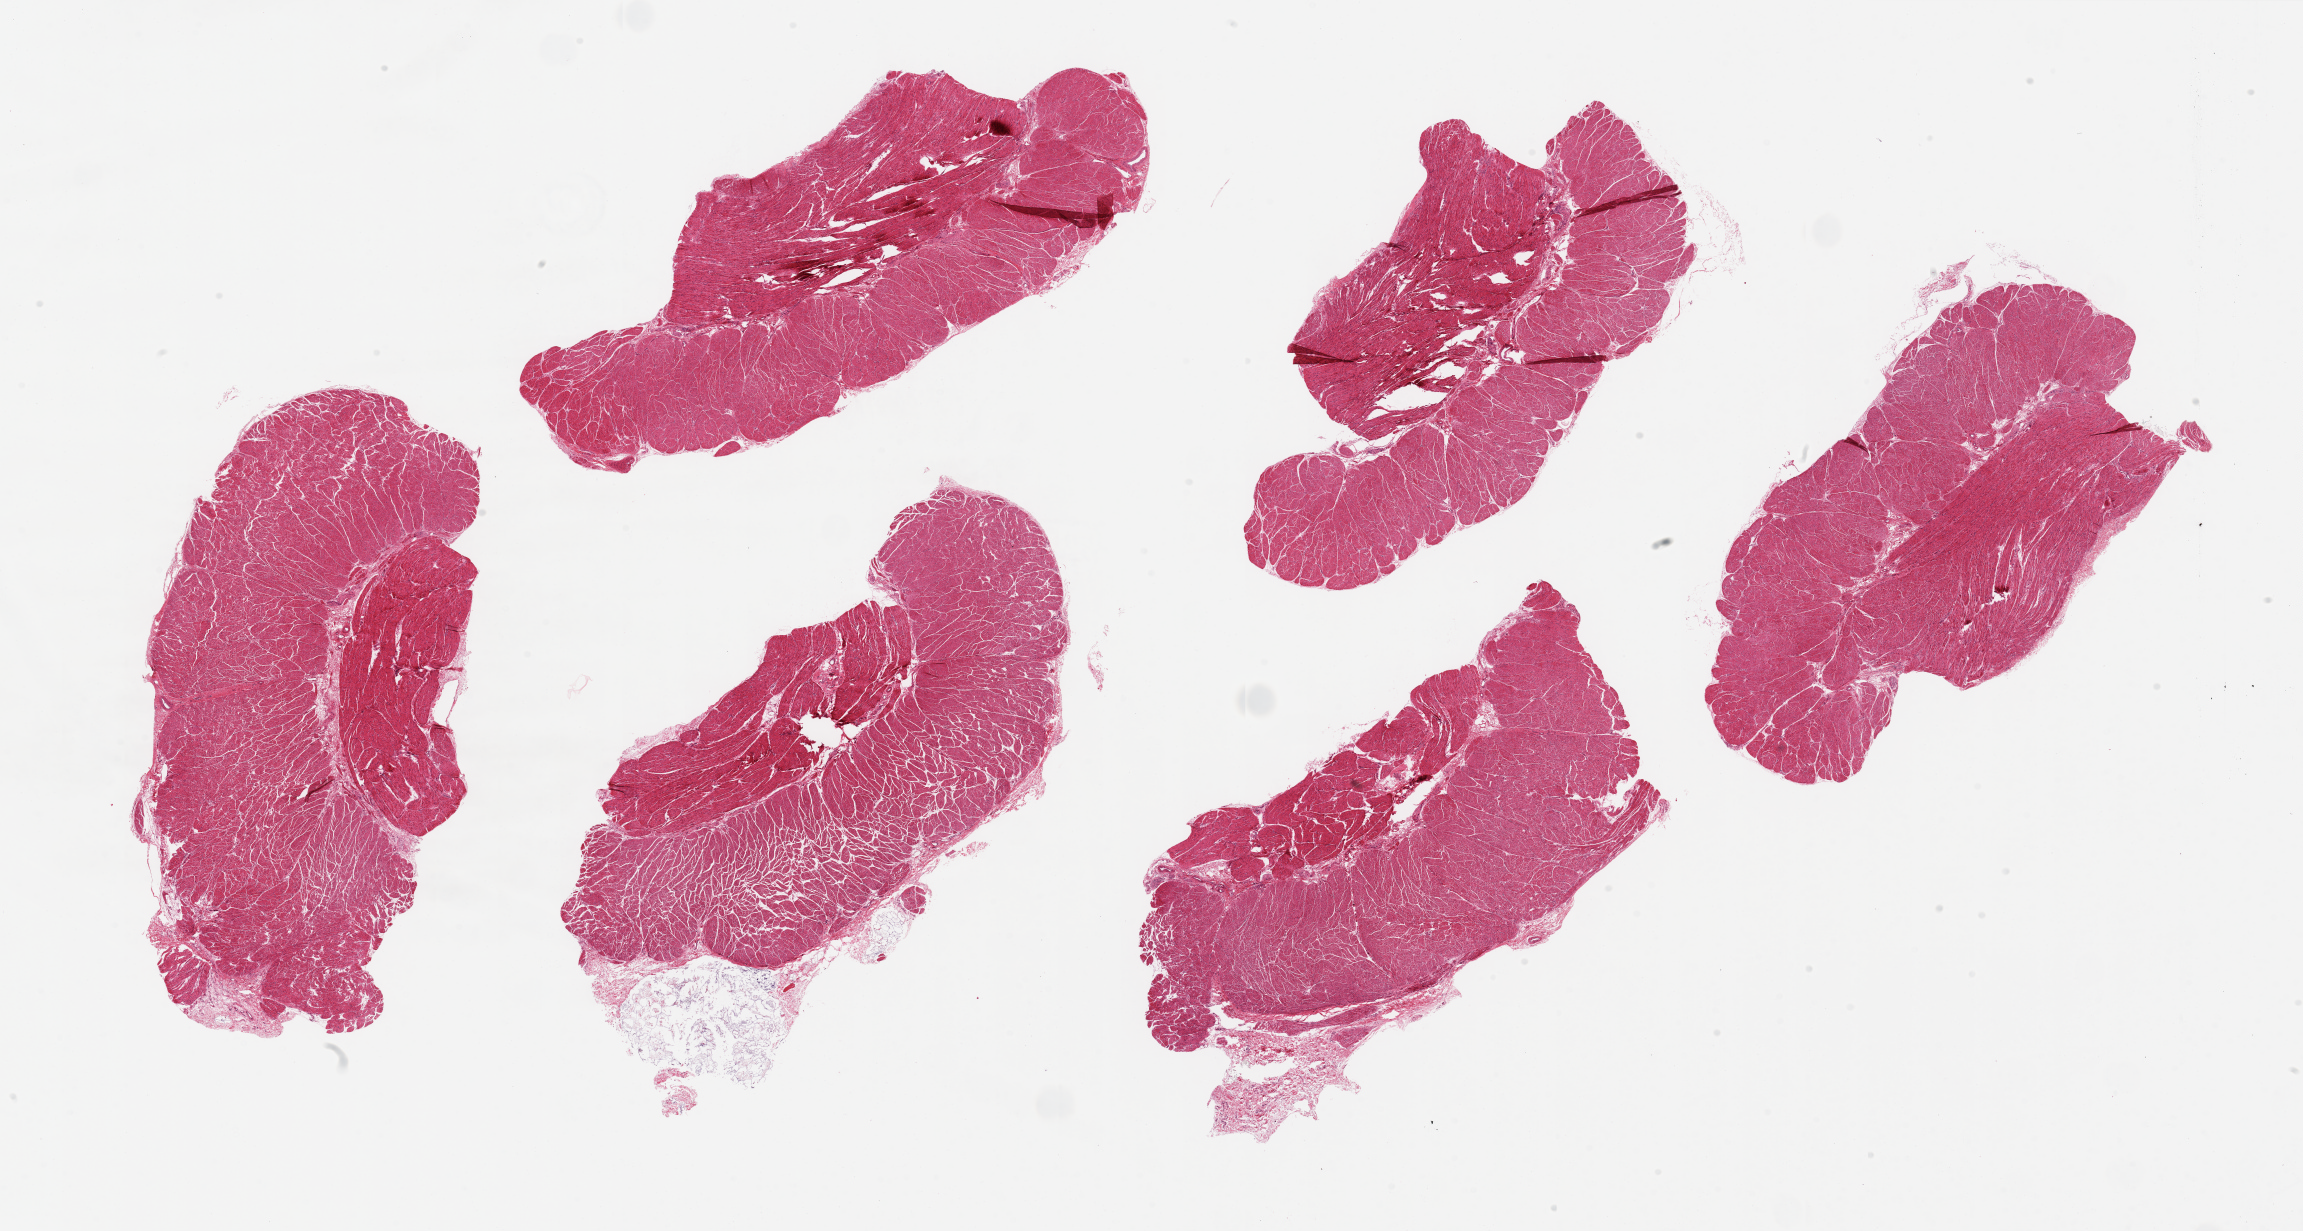
Whole-slide image, H&E stain — shown as a low-resolution overview of the whole scanned area (about 36.4 x 19.5 mm), PAXgene-fixed paraffin-embedded (PFPE) section, target tissue: esophageal muscle, donor tissue sample. Donor: male.
• reviewer comment on this tissue sample: 6 pieces ~9x4mm